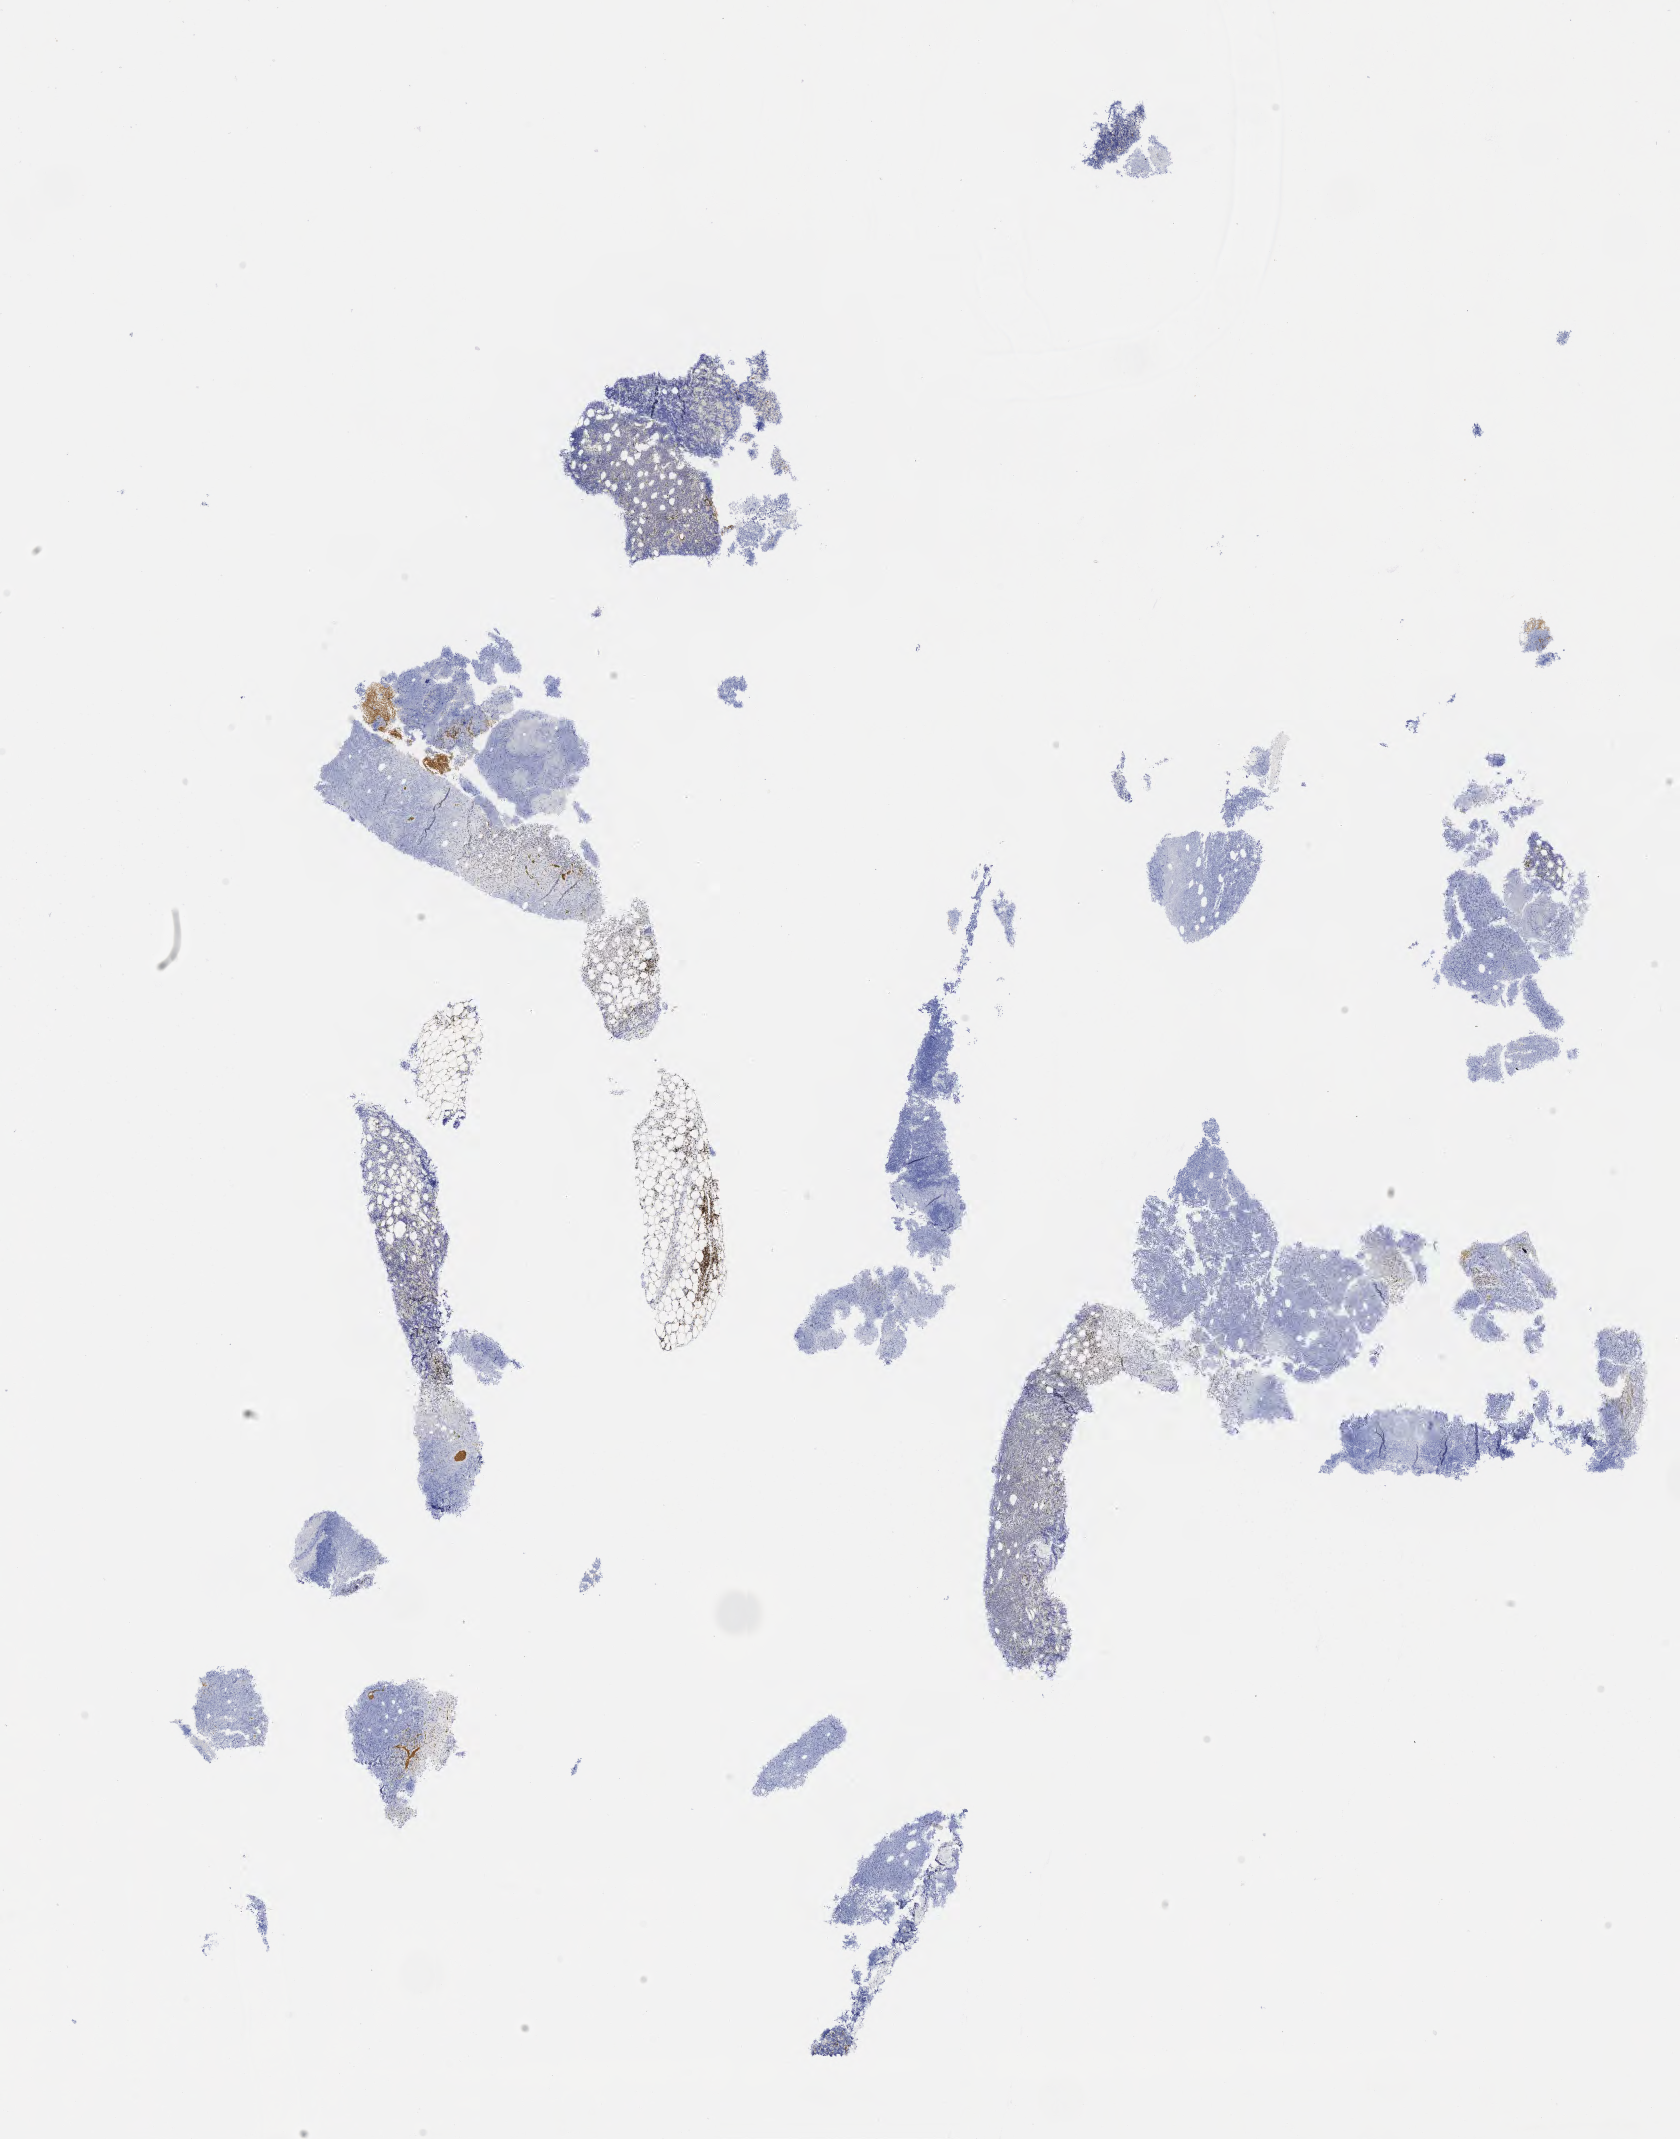
Immunohistochemistry (IHC) whole-slide image stained for BCL2 — a low-resolution overview of the entire scanned area, about 13.6 x 17.3 mm; tumor tissue; site: pelvis. Patient female; 64 years old.
Histologic diagnosis: Burkitt lymphoma, NOS.